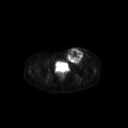
FDG PET of an extremity soft-tissue mass (from a PET/CT study), one axial slice; slice 66 of 267 in the series (ordered by position); 3.27 mm slice thickness; 128 × 128 image matrix, field of view 600 × 600 mm. Female patient, age 24 years. Case-level facts recorded for this patient, not image findings: histological type: leiomyosarcoma; grade: high; site of the primary tumour: groin.
Structures marked on this image (expert contour drawn on MRI and transferred to this co-registered scan by the dataset authors):
- gross tumour volume including surrounding oedema: box from (x=65, y=47) to (x=91, y=64) px
- gross tumour volume (mass): (x=66, y=48)–(x=84, y=64)